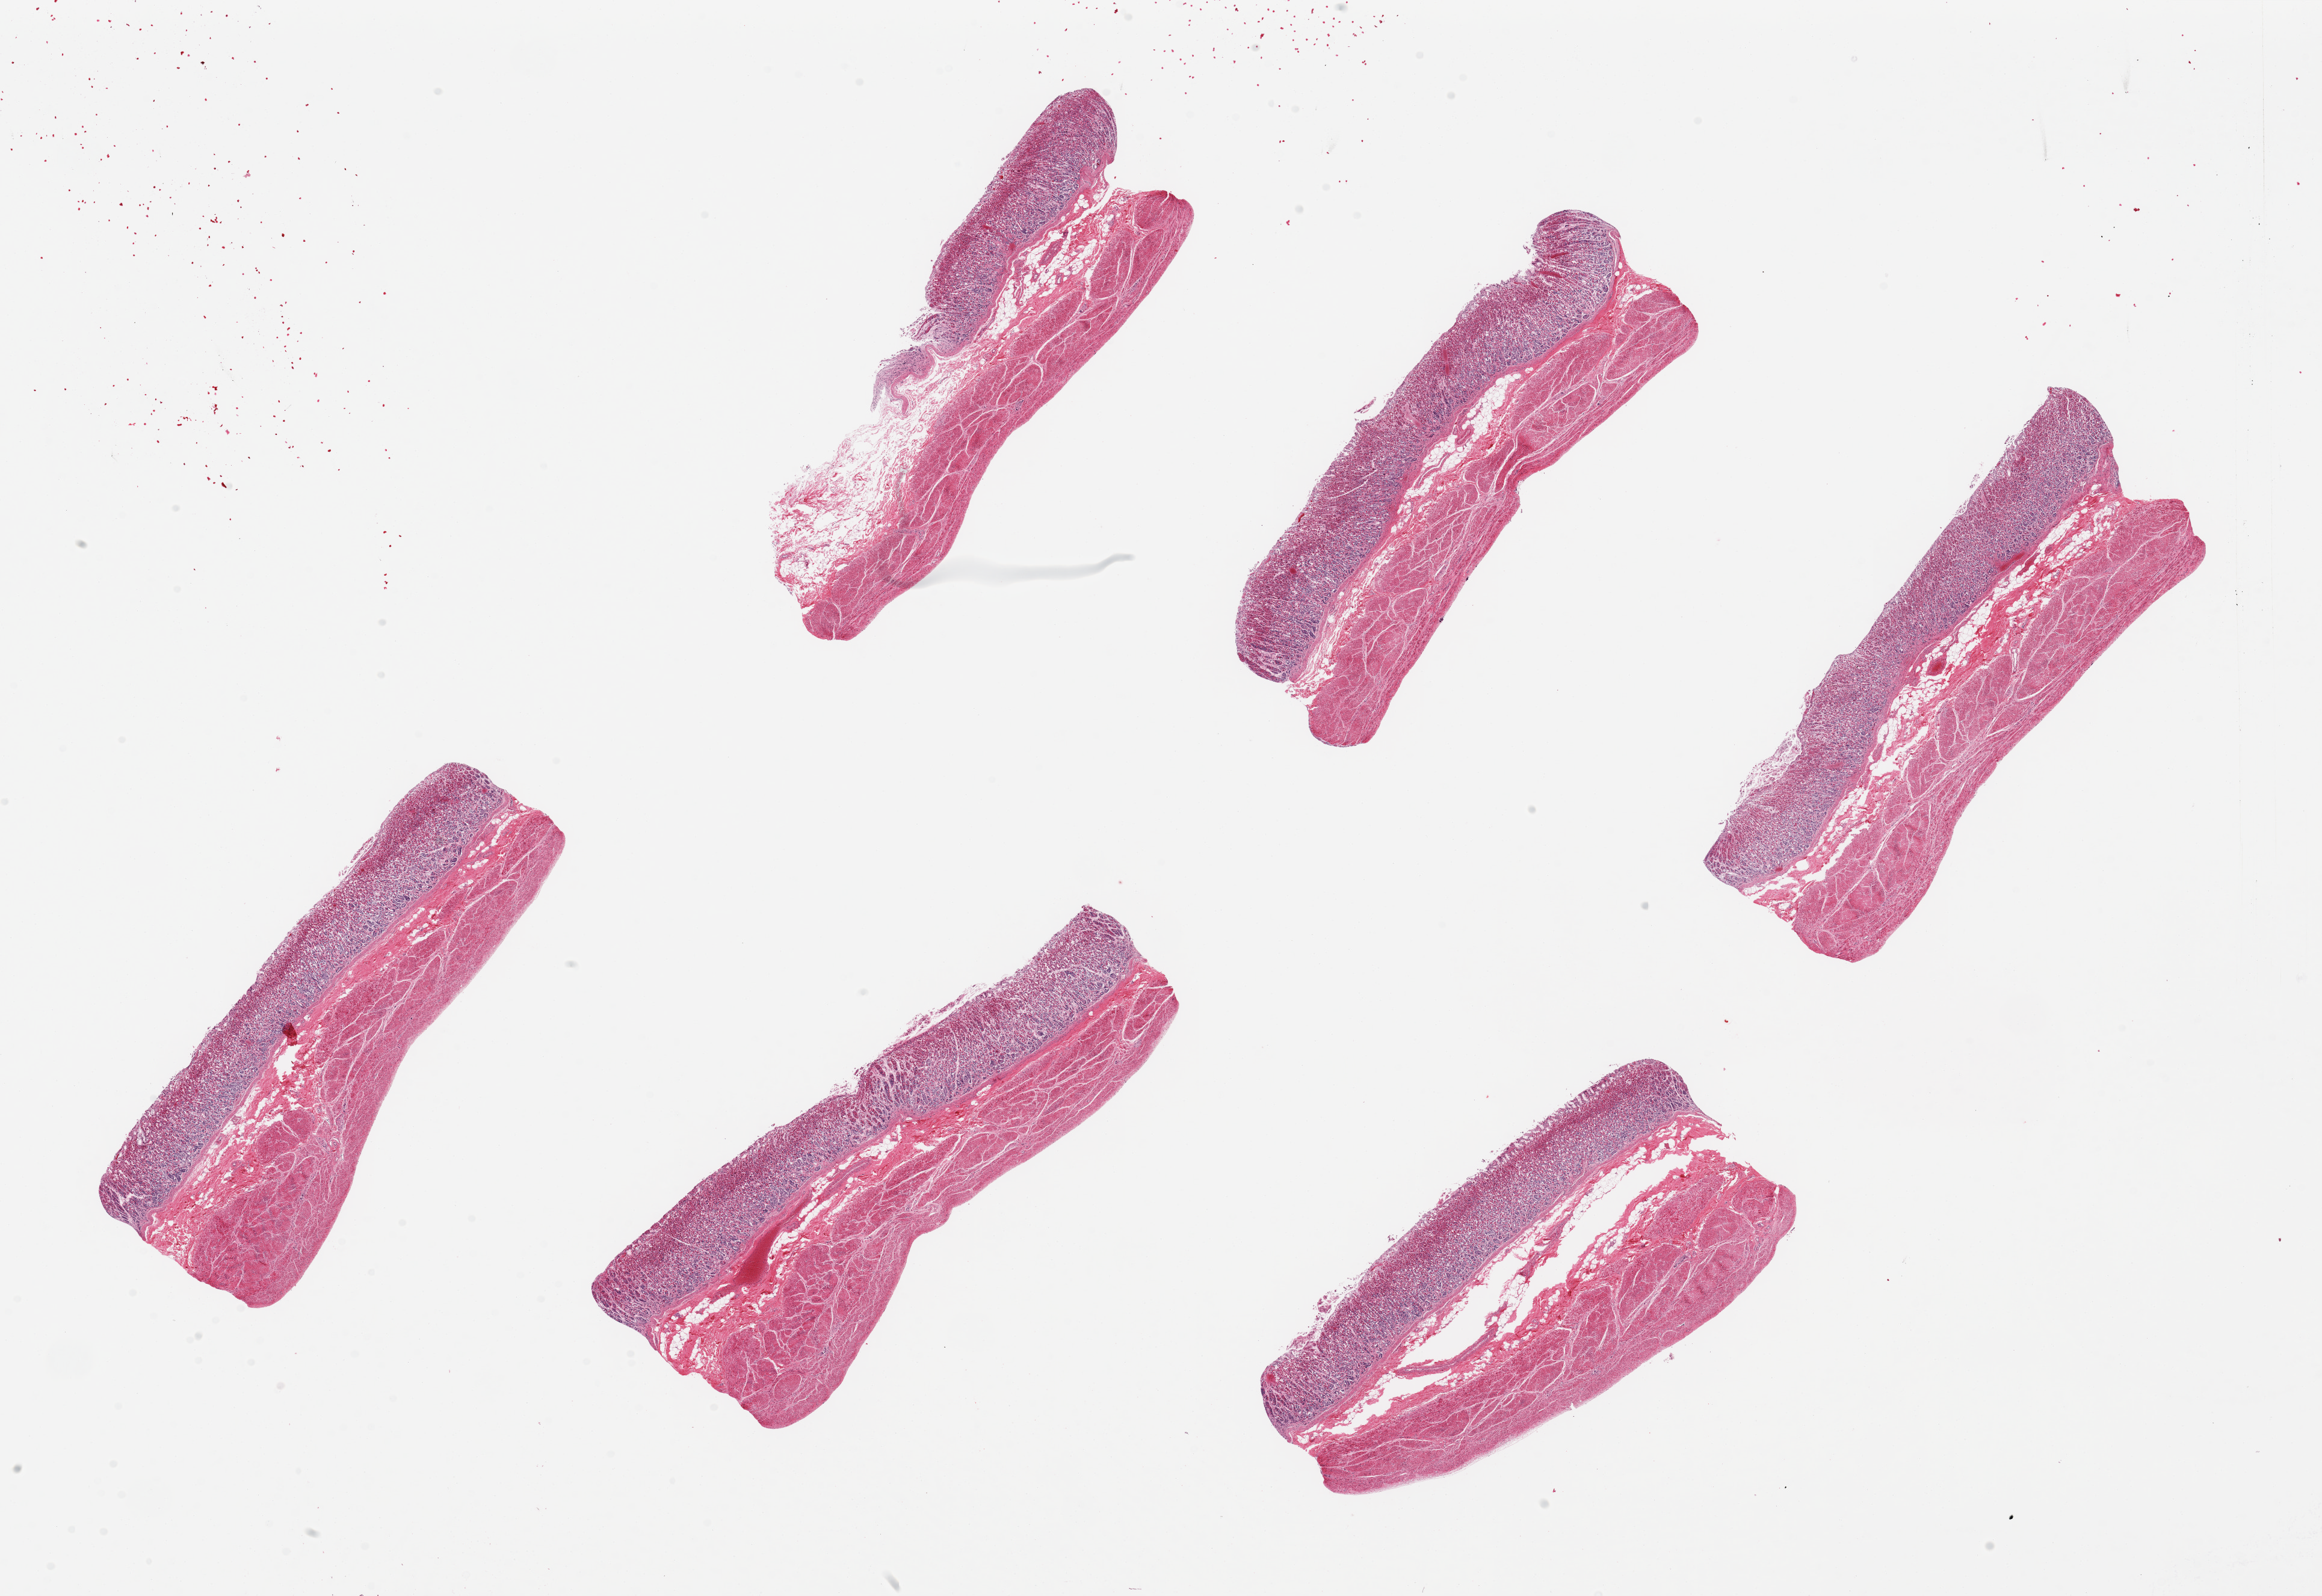
Haematoxylin and eosin whole-slide image, brightfield, whole scanned area (about 30.5 x 21.0 mm, slide scanned at 20x) shown as a low-resolution overview, PAXgene-fixed paraffin-embedded (PFPE) section, target tissue: stomach, donor tissue sample. Donor: male.
Reviewer comment on this tissue sample: 6 pieces up to 8x3 mm; oxyntic mucosa thick, but moderately autolyzed as is muscularis.